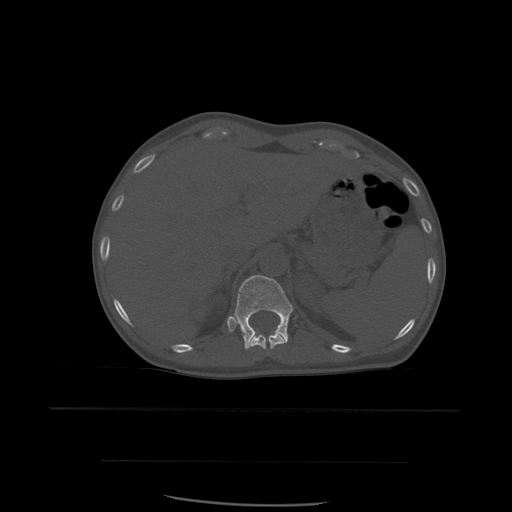
CT including the spine, one axial slice; slice 282 of 574 in the series (ordered by position); bone window (W 1800 / L 400 HU); 1.25 mm slice thickness; 512 × 512 image matrix, field of view 392 × 392 mm. Patient age 48 years. From the clinical record (not read from this slice): primary cancer: lung; vertebrae with lytic lesions (as recorded): T11.
Structures marked on this image (semi-automatic segmentation, software-assisted and operator-edited):
- T11 vertebra: box from (x=250, y=332) to (x=287, y=350) px
- T12 vertebra: (x=234, y=275)–(x=293, y=350)